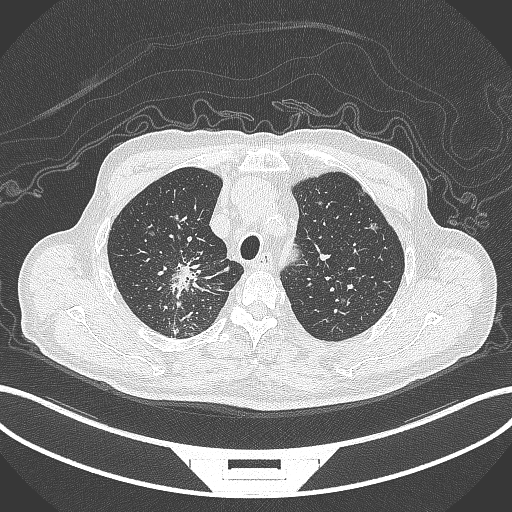
Chest CT, one axial slice; position 301 of 407 along the scan axis; reconstruction kernel B70f; lung window (W 1500 / L -600 HU); 1 mm slice thickness; 512 × 512 image matrix. Male patient, age 69 years. Case-level facts recorded for this patient, not image findings: clinical TNM (as recorded): T1c N1 M1.
Outlined on this slice (bounding box drawn by a radiologist):
- lung tumour (recorded histology: adenocarcinoma): bounding box (x1, y1, x2, y2) in pixels: (169, 254, 212, 306)